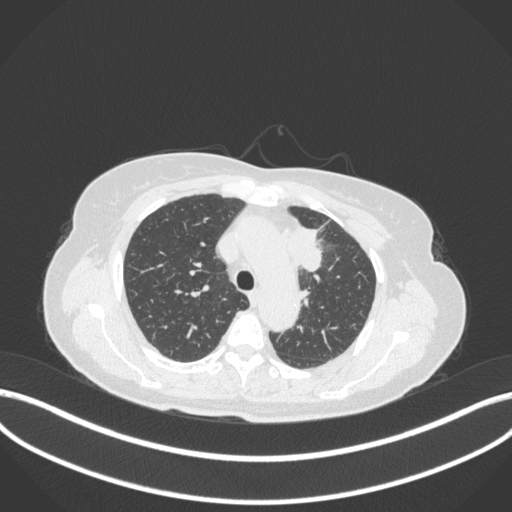
Chest CT, one axial slice. Slice 245 of 368 in the series (ordered by position). Reconstruction kernel B31f. 120 kVp. Lung window (W 1500 / L -600 HU). 512 × 512 image matrix. Female patient, age 65 years. From the clinical record (not read from this slice): clinical TNM (as recorded): T2a N0 M0.
Structures marked on this image (rectangle marked by the reading radiologist):
- lung tumour (recorded histology: adenocarcinoma): bounding box (x1, y1, x2, y2) in pixels: (287, 224, 326, 276)